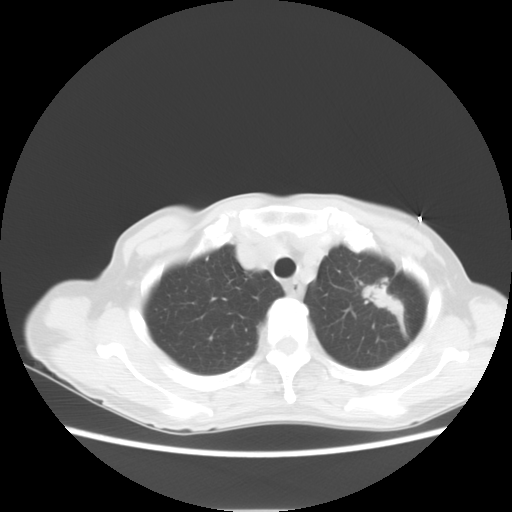
Chest CT, one axial slice. Position 11 of 14 along the scan axis. Reconstruction kernel STANDARD. 120 kVp. Lung window (W 1500 / L -600 HU). 5 mm slice thickness. 512 × 512 image matrix, field of view 350 × 350 mm. Patient: female, 71 years. Case-level facts recorded for this patient, not image findings: clinical TNM (as recorded): T2 N0 M0.
Outlined on this slice (bounding box drawn by a radiologist):
- lung tumour (recorded histology: adenocarcinoma): box from (x=363, y=279) to (x=407, y=321) px